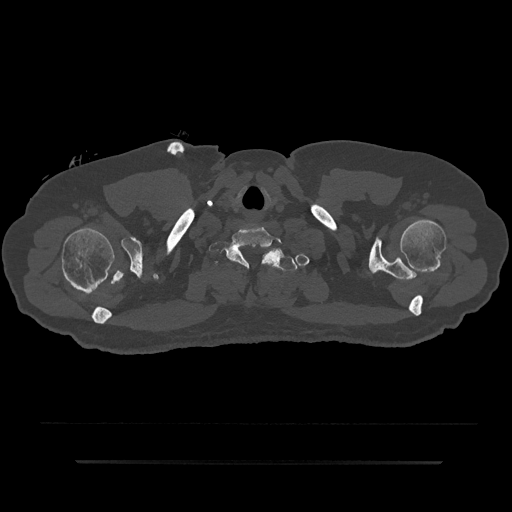
CT including the spine, one axial slice; position 761 of 797 along the scan axis; reconstruction kernel Br40s/3; bone window (W 1800 / L 400 HU); 512 × 512 image matrix. Male patient, age 59 years. From the clinical record (not read from this slice): primary cancer: bile ducts.
Outlined on this slice (semi-automatic segmentation, software-assisted and operator-edited):
- T1 vertebra: bounding box <214,251,300,271> (left, top, right, bottom; pixels)